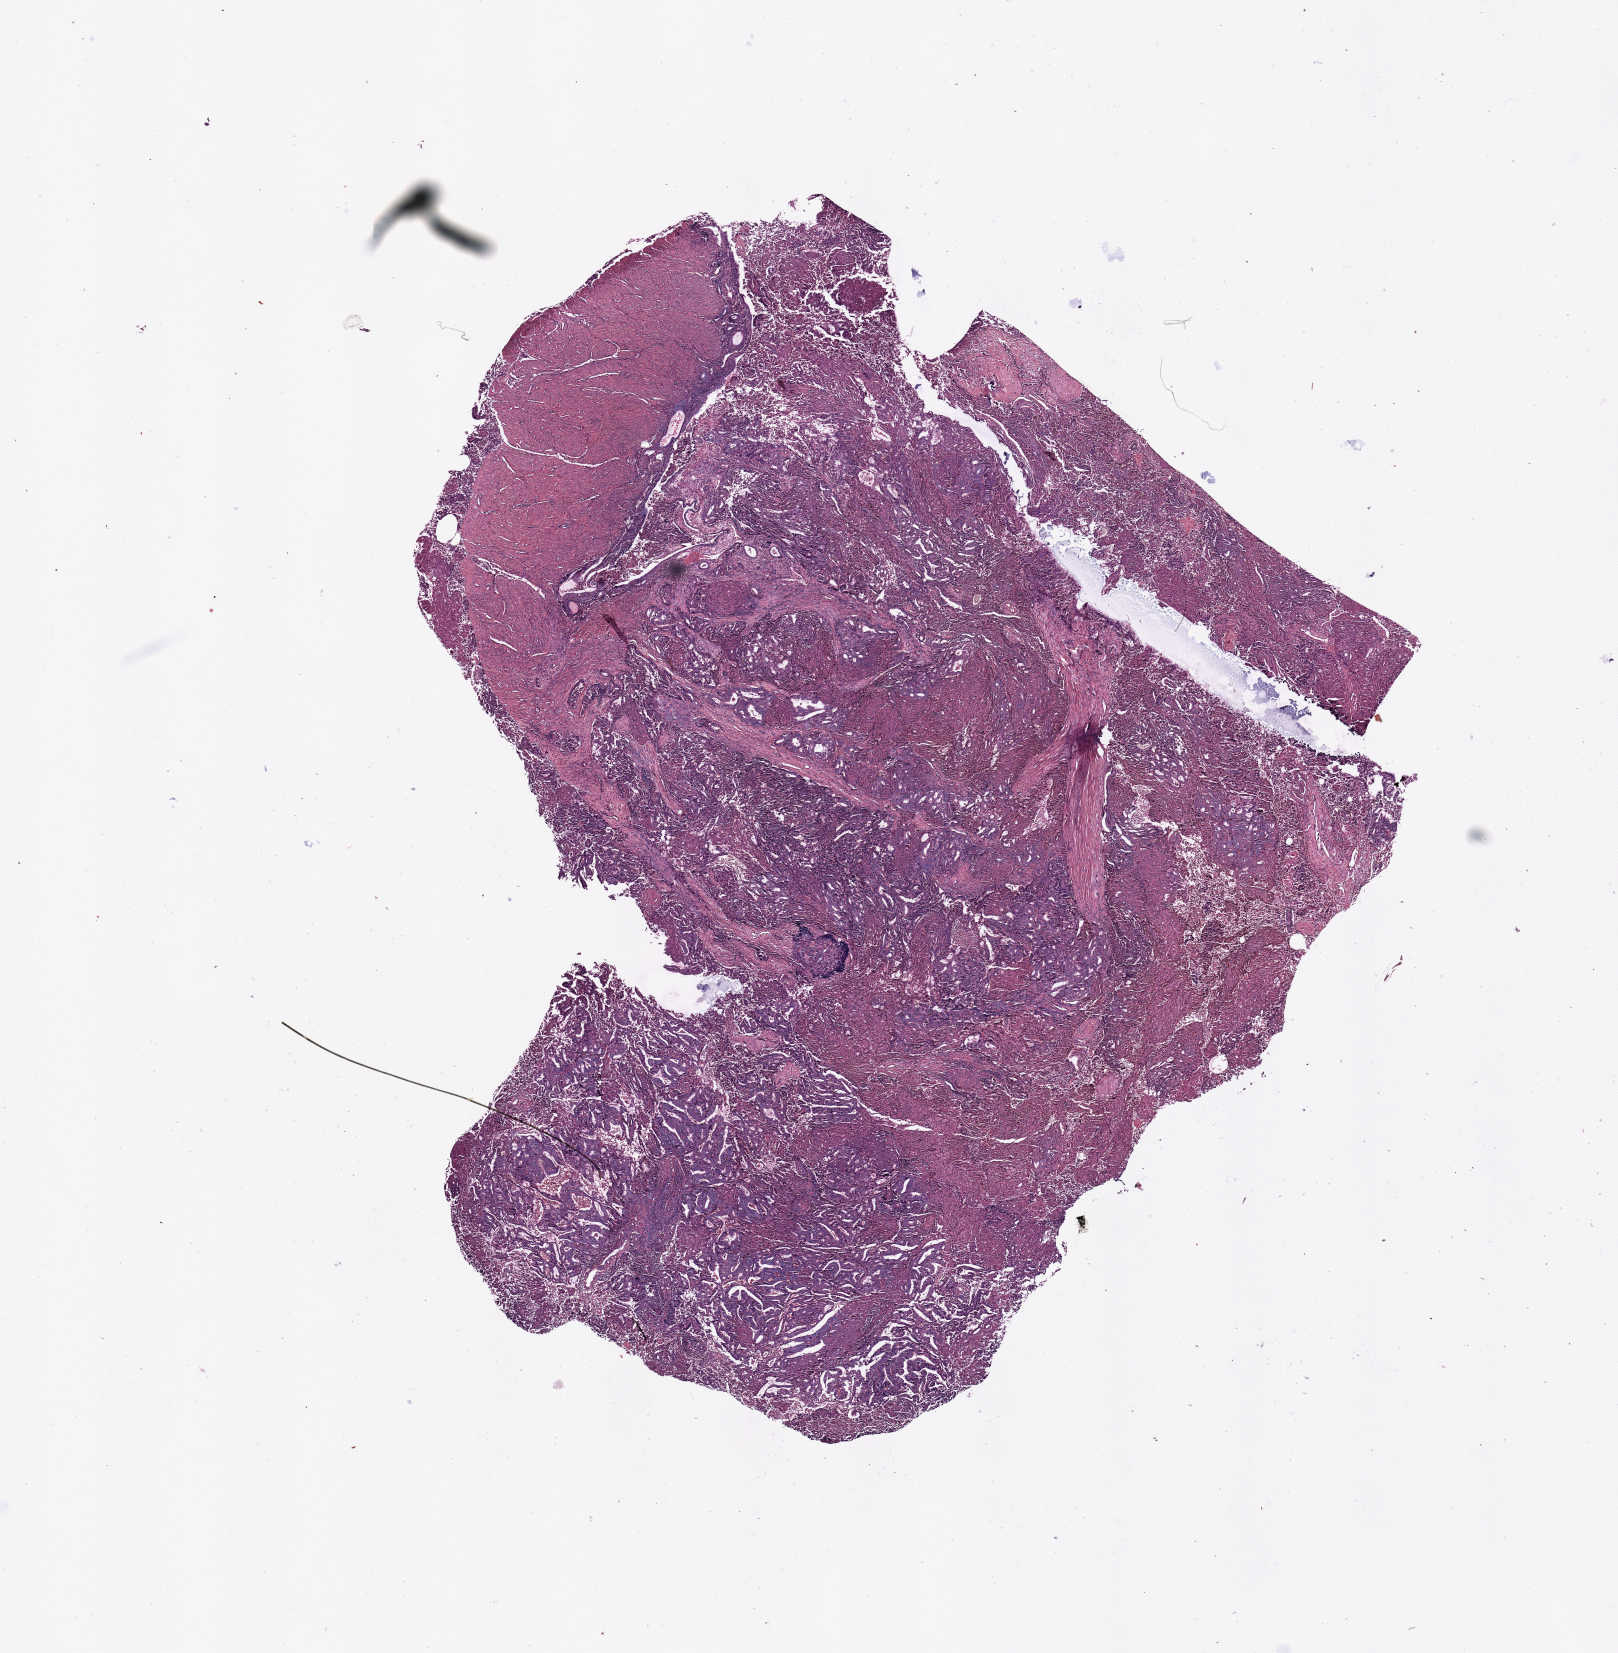
Whole-slide histology image, H&E — whole scanned area (about 12.8 x 13.1 mm) shown as a low-resolution overview. Tumour tissue sample, sampled site: uterus. 57-year-old female patient. Histologic grade: G2 (moderately differentiated). Composition of this section per pathologist review: tumour nuclei 85%, necrosis 0%.
AJCC pathologic stage: III. Histologic diagnosis: Endometrioid adenocarcinoma, NOS.